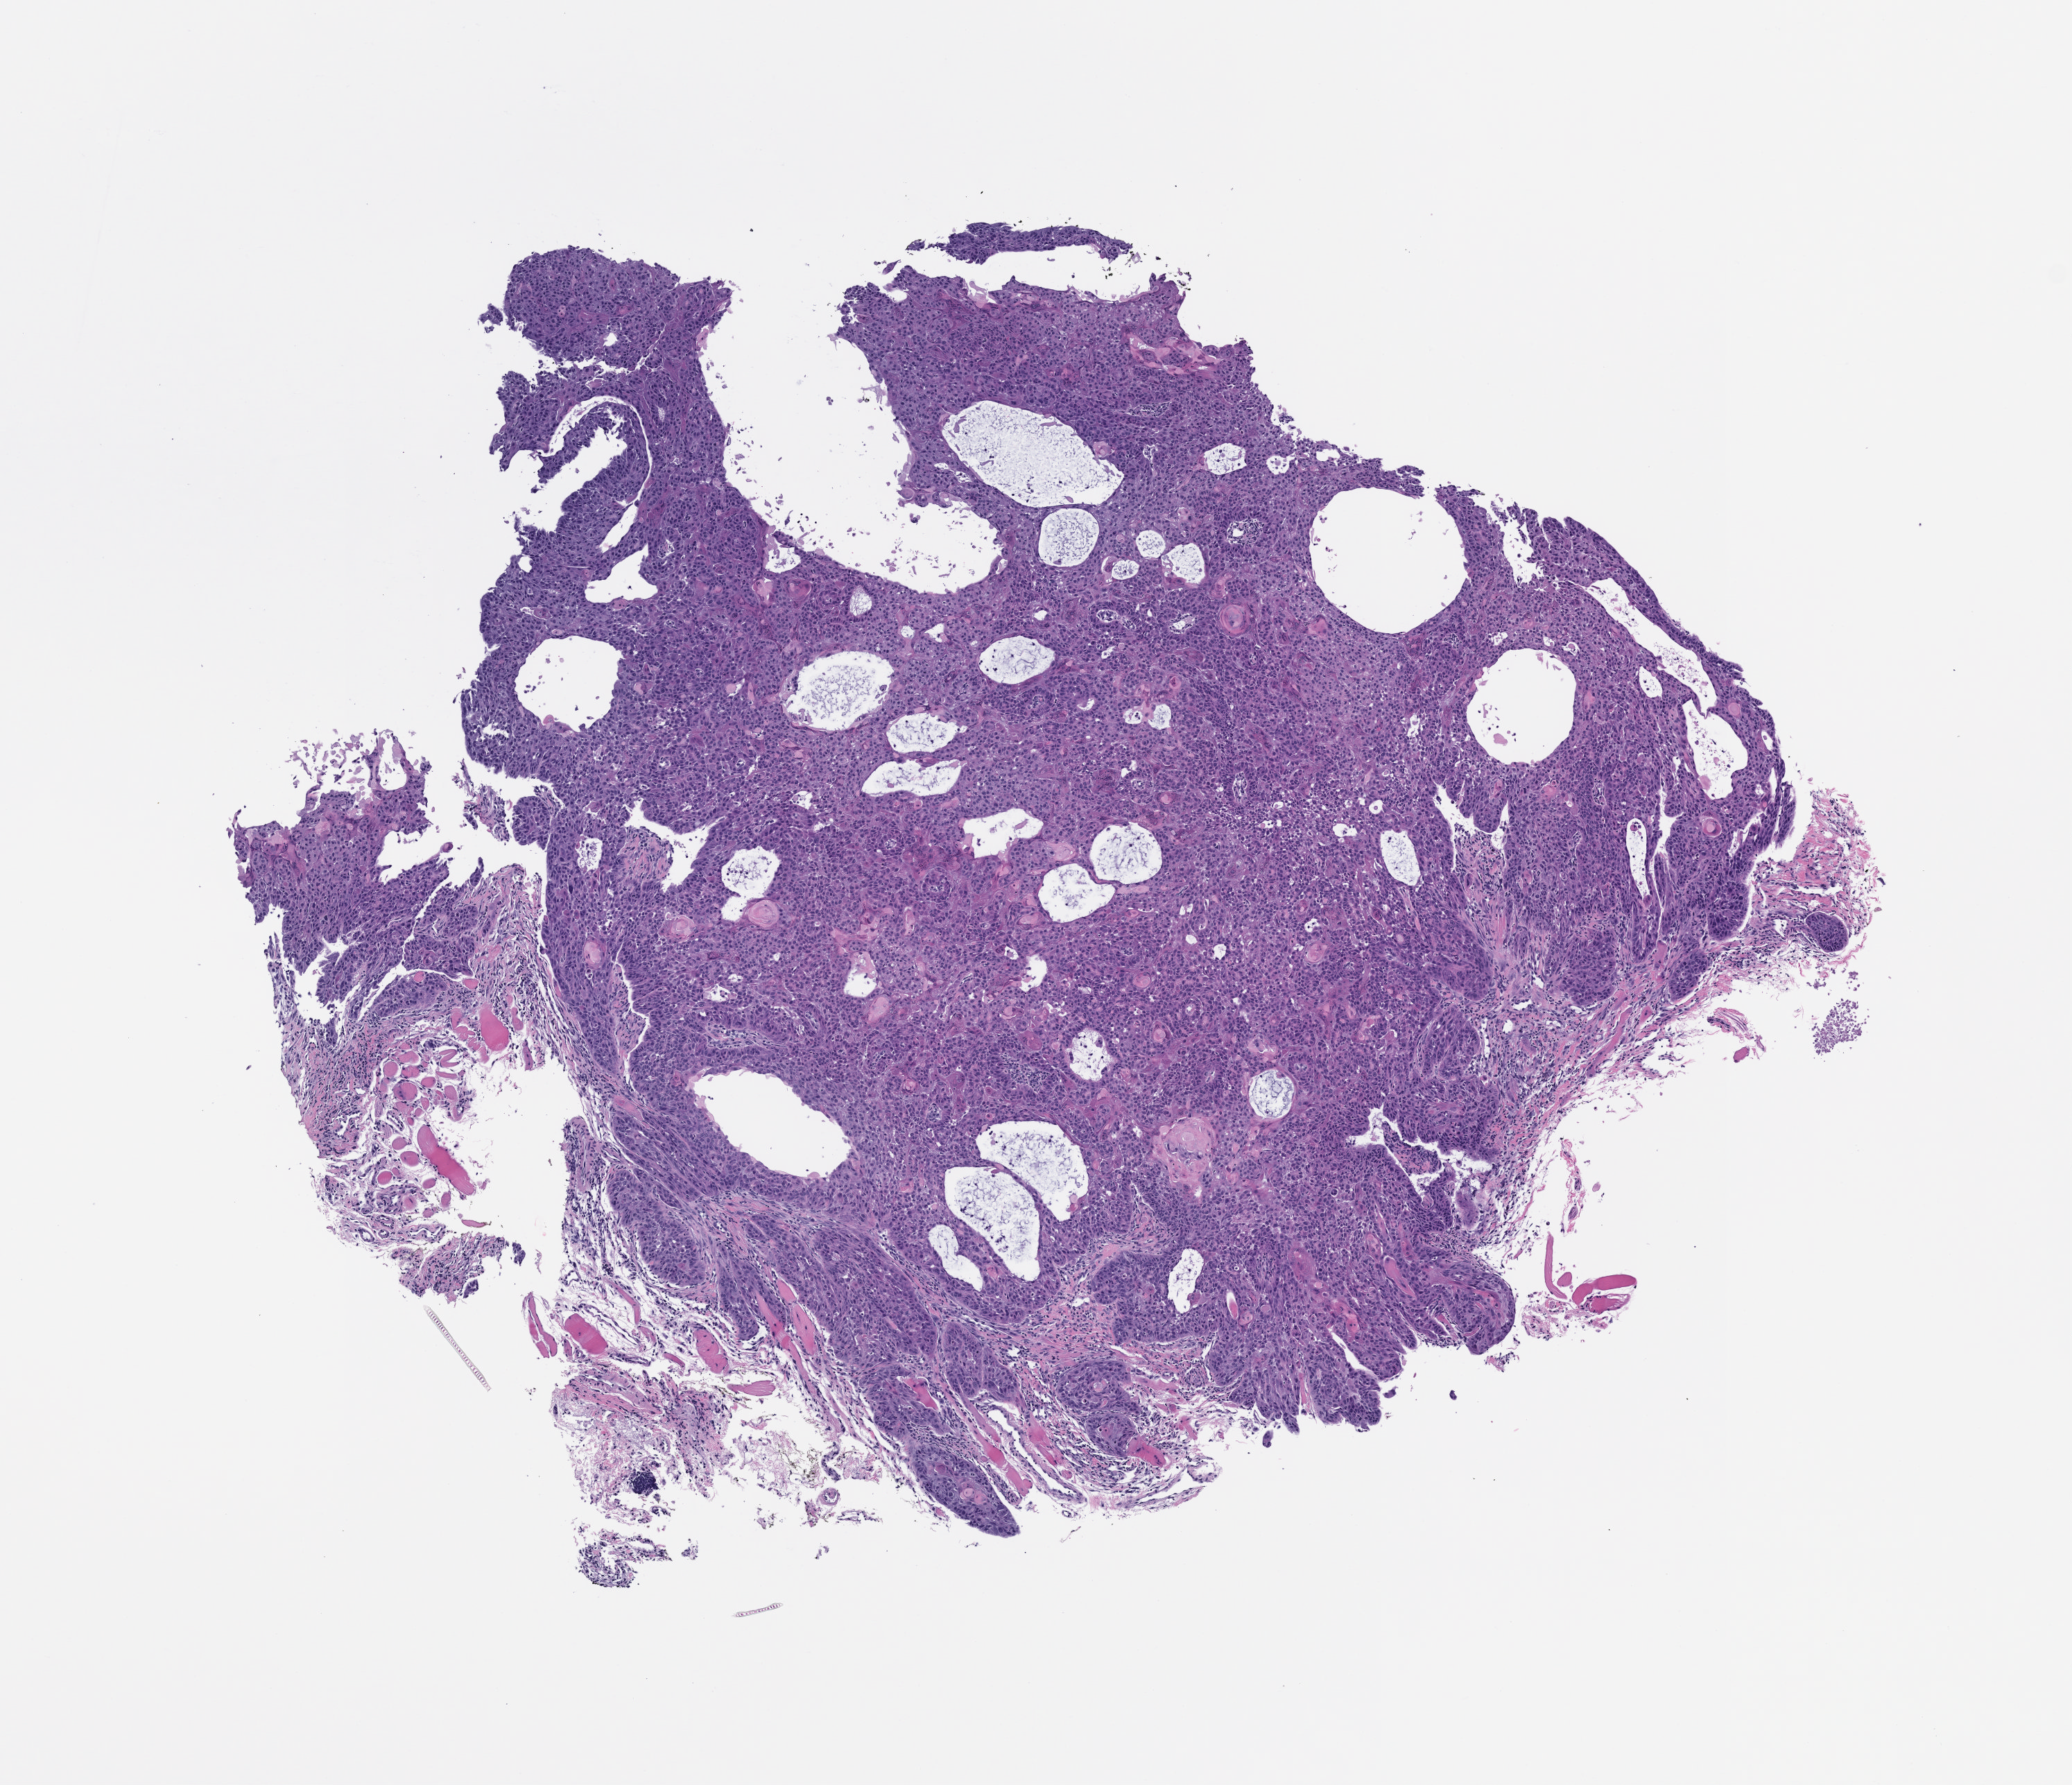
Hematoxylin and eosin (H&E) whole-slide image of a patient-derived xenograft (PDX) tumor grown in a mouse, shown as a low-resolution overview of the whole scanned area (about 6.0 x 5.2 mm); FFPE section; tumor site category: larynx.
* originating patient diagnosis: Head and Neck Squamous Cell Carcinoma